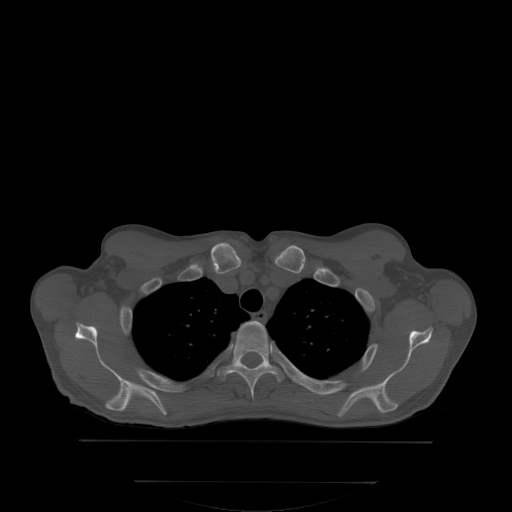
CT including the spine, one axial slice. Bone window (W 1800 / L 400 HU). 2.5 mm slice thickness. 512 × 512 image matrix, field of view 500 × 500 mm. Male patient, age 58 years. From the clinical record (not read from this slice): primary cancer: prostate; vertebrae with lytic lesions (as recorded): L1.
Annotated regions visible in this slice (semi-automatically segmented with operator editing):
- T3 vertebra: bounding box <217,323,295,397> (left, top, right, bottom; pixels)